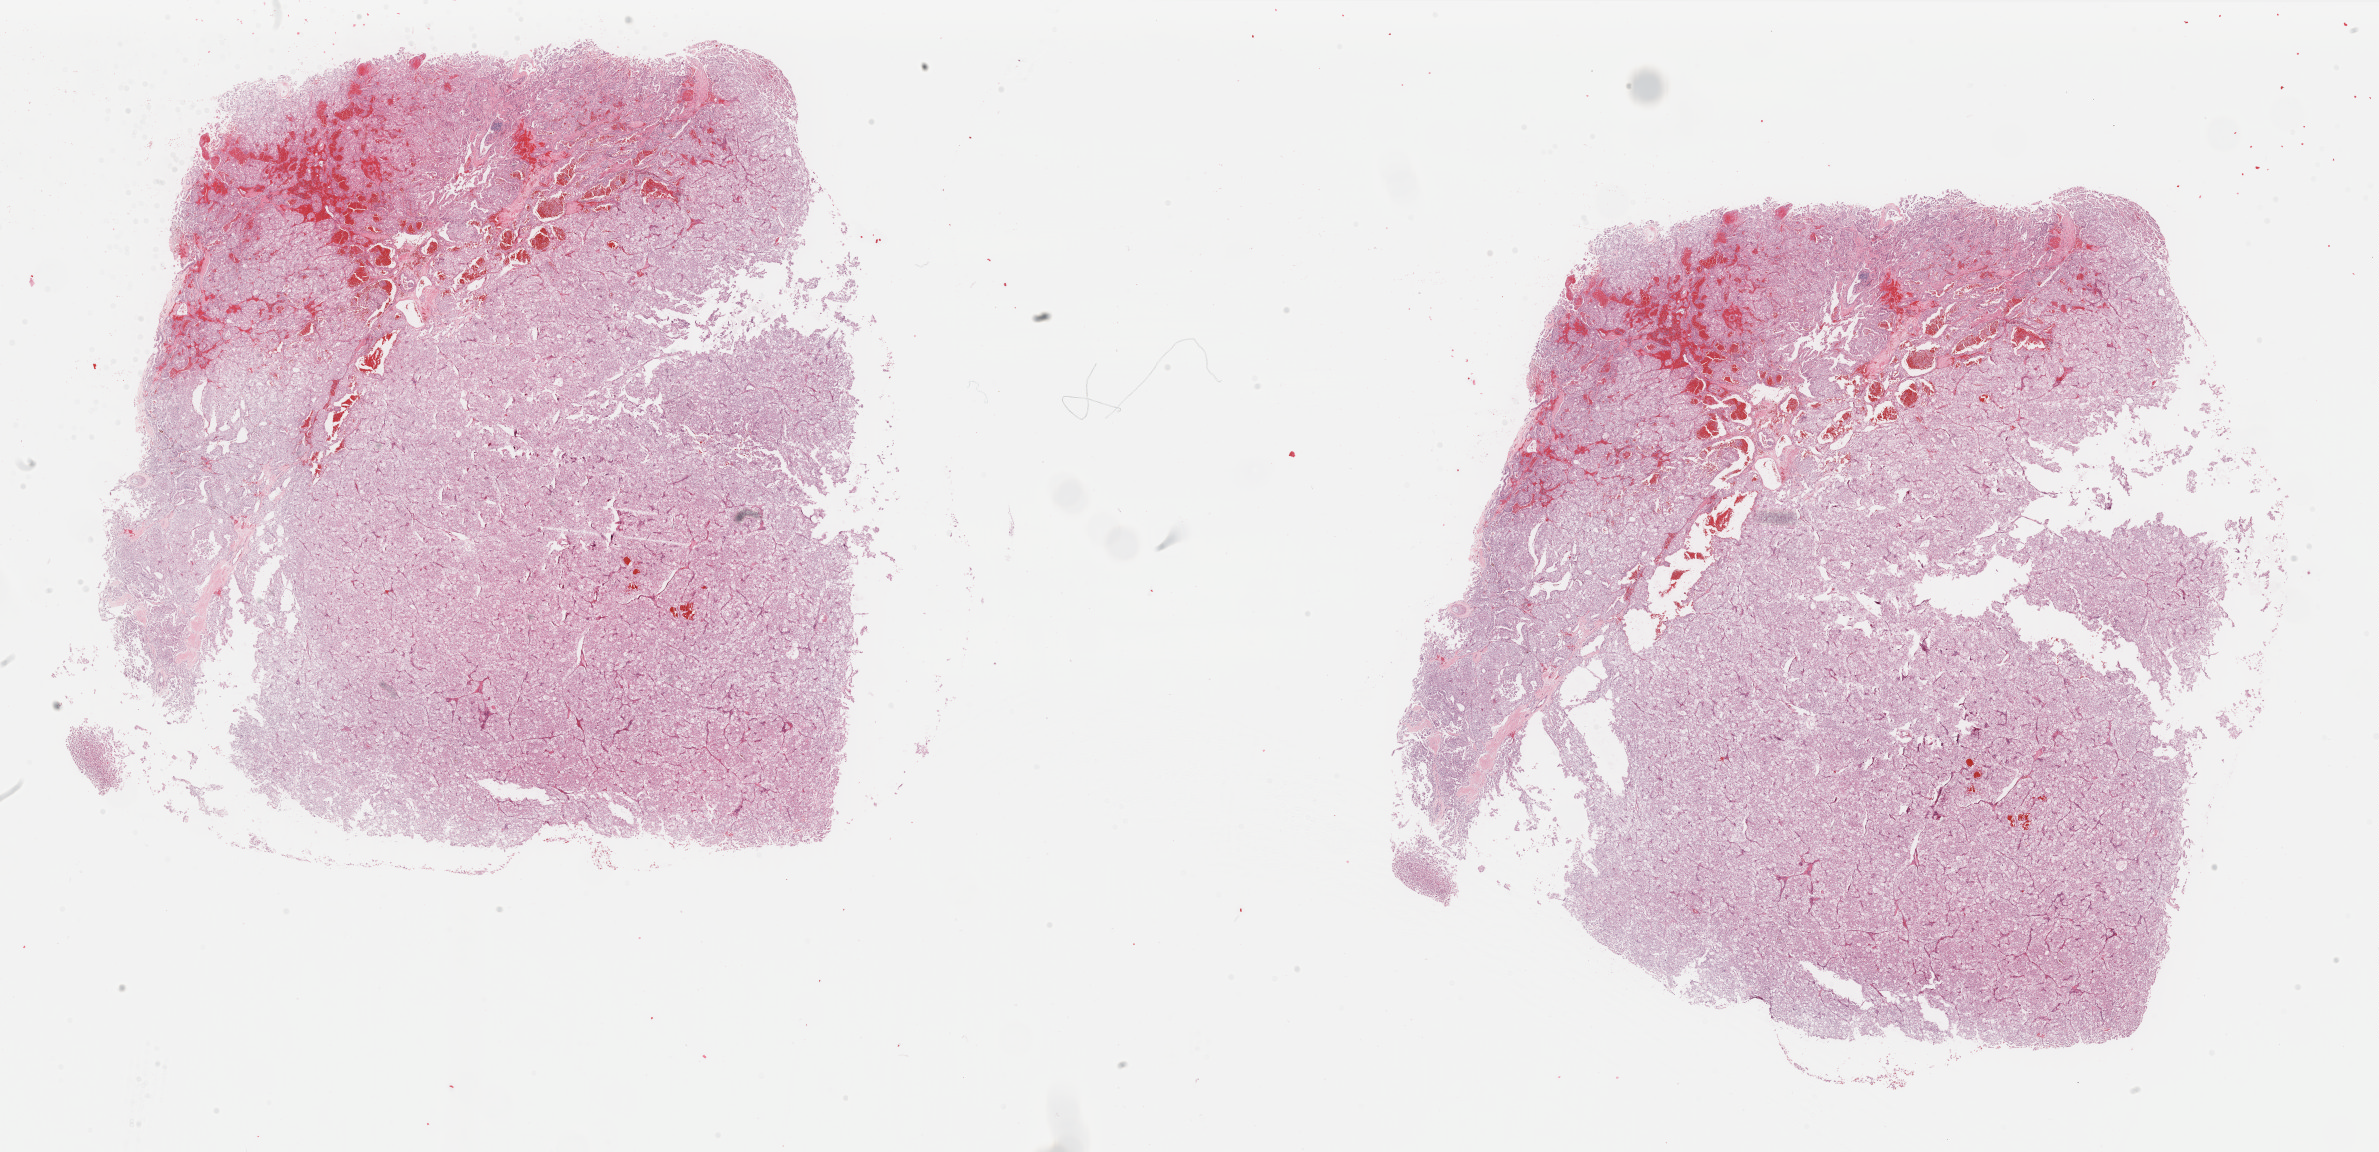
Whole-slide histology image, H&E — shown as a low-resolution overview of the whole scanned area (about 37.7 x 18.2 mm, slide scanned at 40x). Formalin-fixed paraffin-embedded (FFPE) diagnostic section. Primary tumour sample from the kidney. Female patient; age at initial diagnosis 42 years.
Diagnosis: Renal cell carcinoma, chromophobe type.